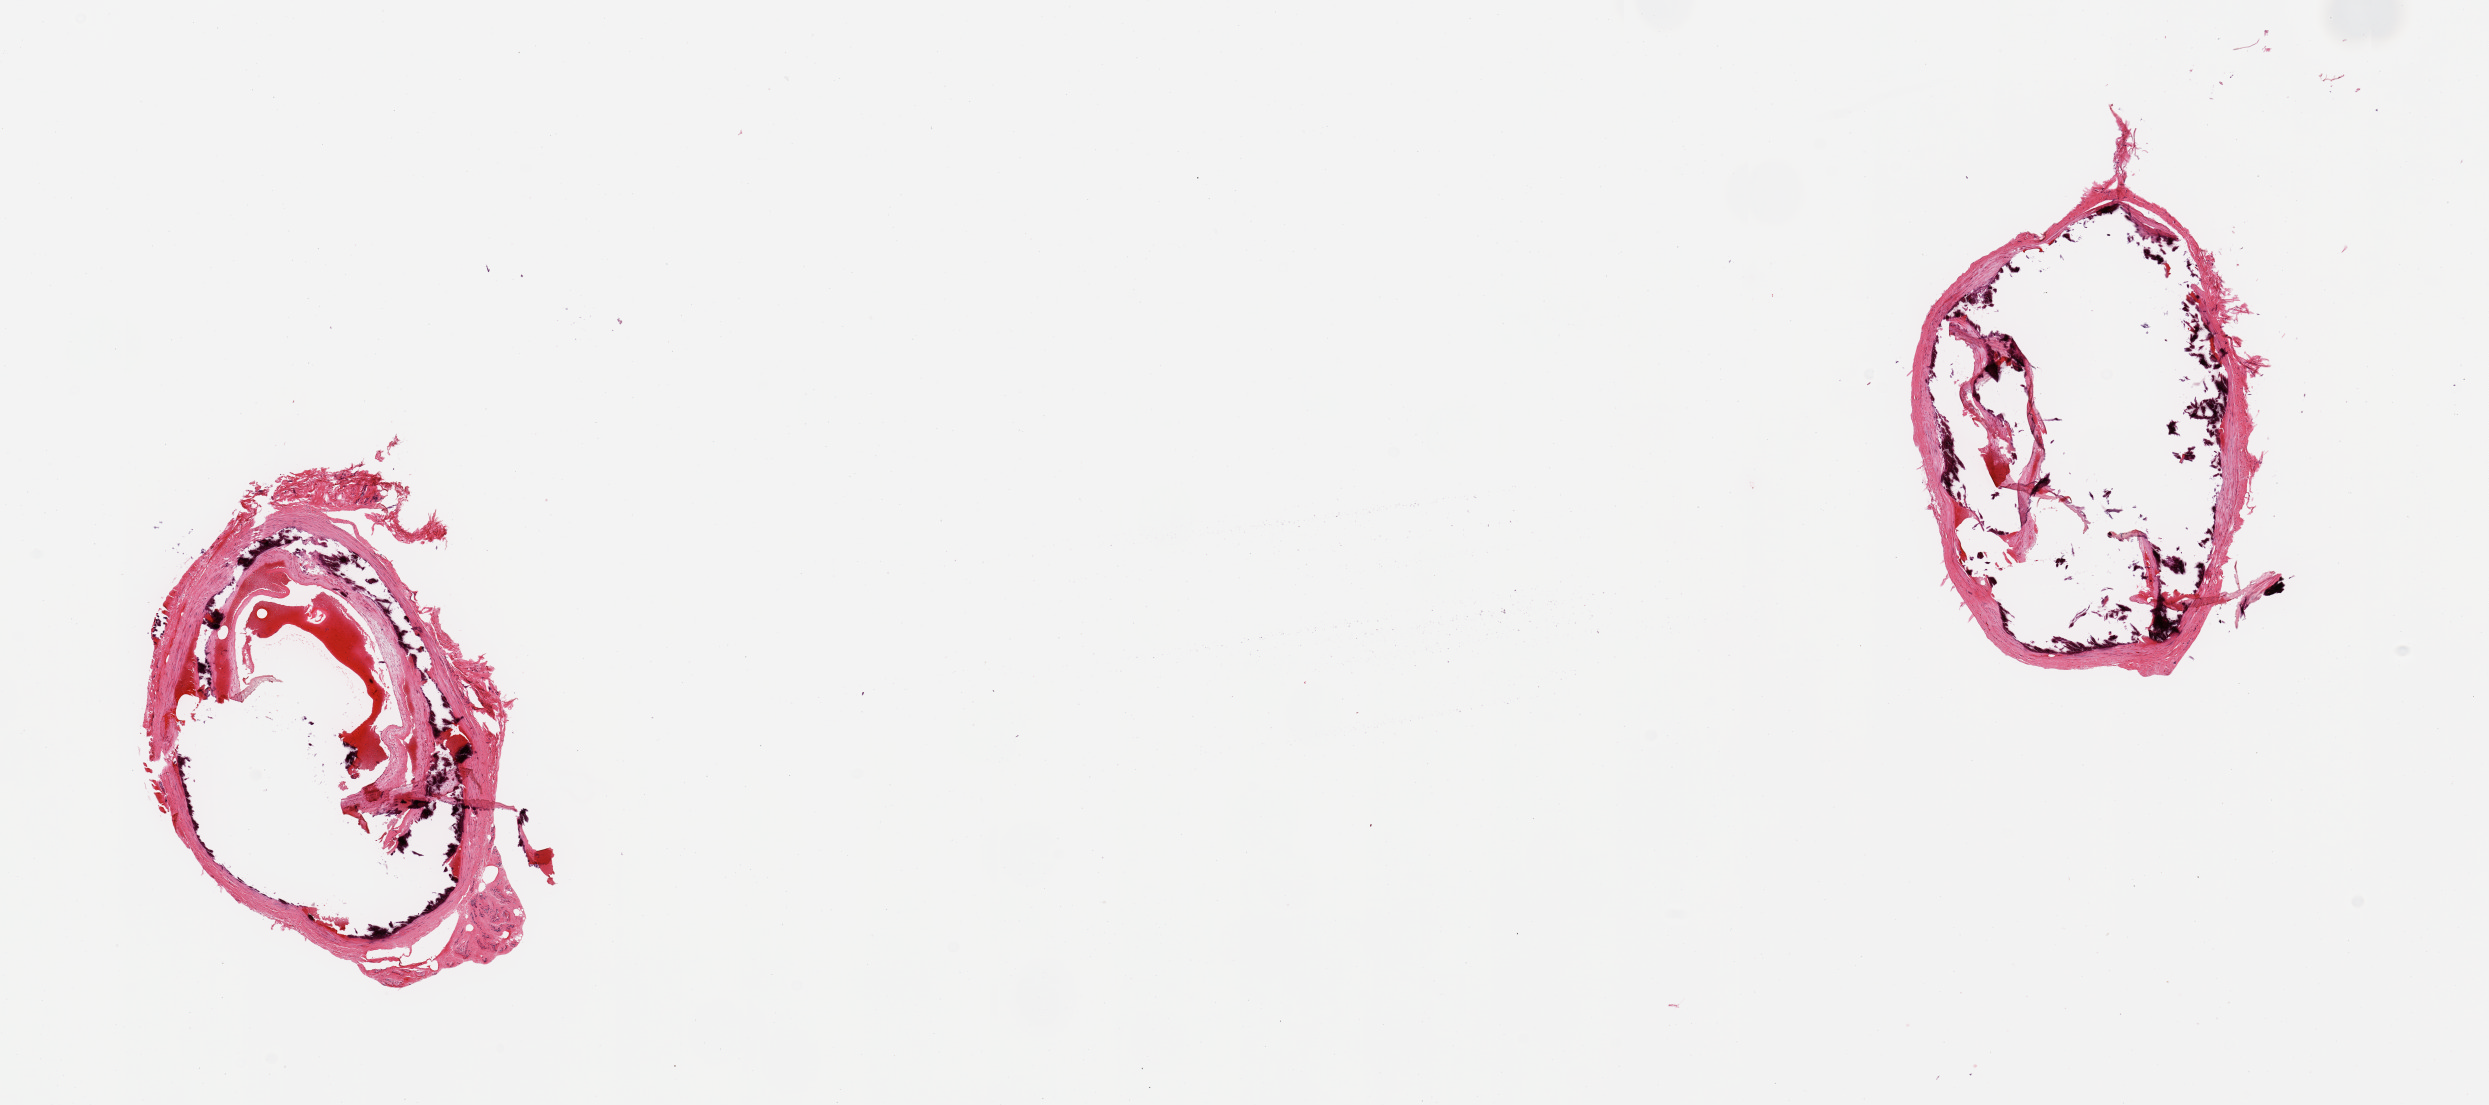
Whole-slide image, hematoxylin and eosin (H&E) stain, a low-resolution overview of the entire scanned area, about 19.7 x 8.7 mm; PAXgene-fixed, paraffin-embedded tissue; section of tibial artery (target tissue); tissue donor sample.
Reviewer comment on this tissue sample: 2 pieces; fragmented, medial calcific sclerosis, atherosclerosis.